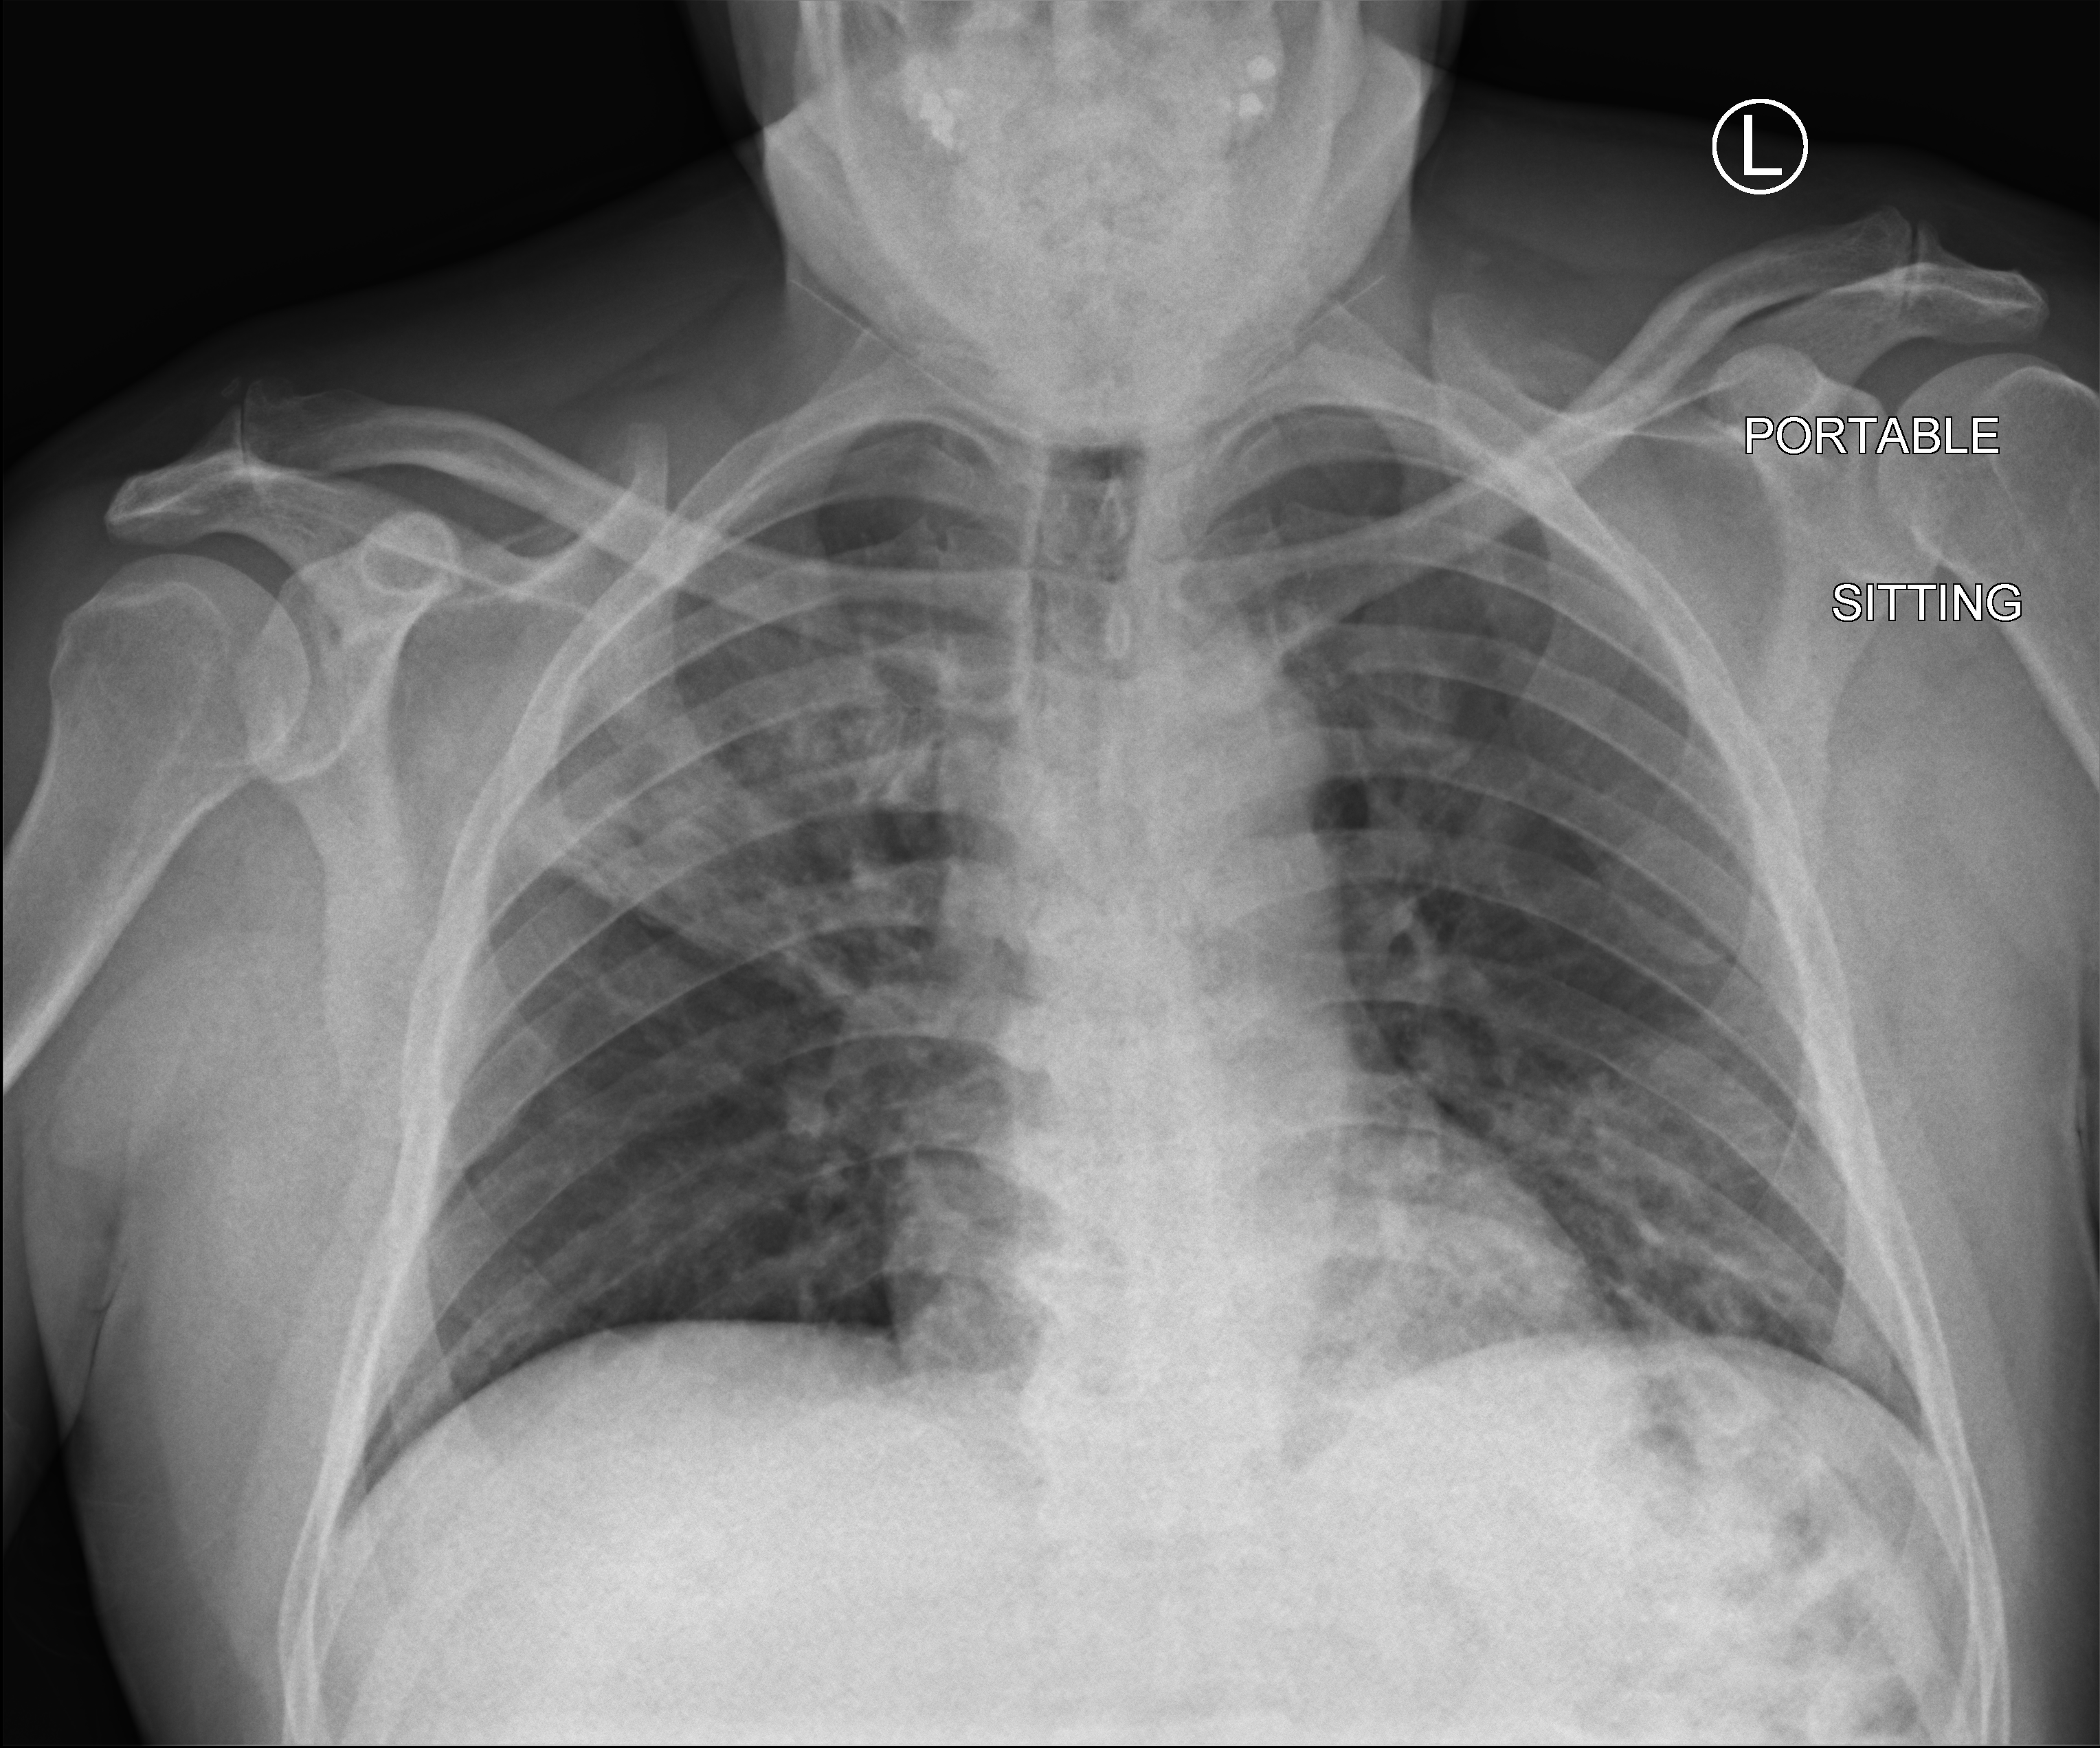
Chest X-ray (portable). Male patient hospitalised with COVID-19, age 18–59 years.
From the hospital-stay record, not from the radiograph (when in the stay this image was taken is not recorded): chronic kidney disease (admission record): no; mechanically ventilated during this hospital stay: no; admitted to intensive care during this hospital stay: no.